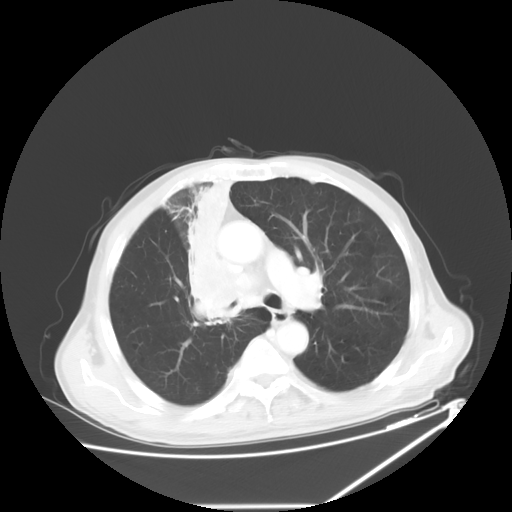
Chest CT, one axial slice; slice 39 of 60 in the series (ordered by position); reconstruction kernel STANDARD; lung window (W 1500 / L -600 HU); 5 mm slice thickness; 512 × 512 image matrix, field of view 410 × 410 mm. Patient: male, 73 years. From the clinical record (not read from this slice): clinical TNM (as recorded): T2a N1 M0.
Annotated regions visible in this slice (bounding box drawn by a radiologist):
- lung tumour (recorded histology: squamous cell carcinoma): bounding box [x1, y1, x2, y2] px = [184, 182, 253, 327]